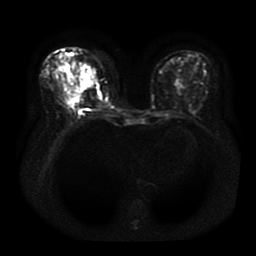
Breast MRI, one axial slice; position 15 of 41 along the scan axis; diffusion-weighted series; image 2 of 4 stored at this slice position (different b-values; order by instance number); 1.5 T; 5 mm slice thickness; 256 × 256 image matrix, field of view 330 × 330 mm. Female patient.
Structures marked on this image (manually delineated by an expert):
- tumour on diffusion-weighted imaging: box from (x=69, y=88) to (x=75, y=91) px